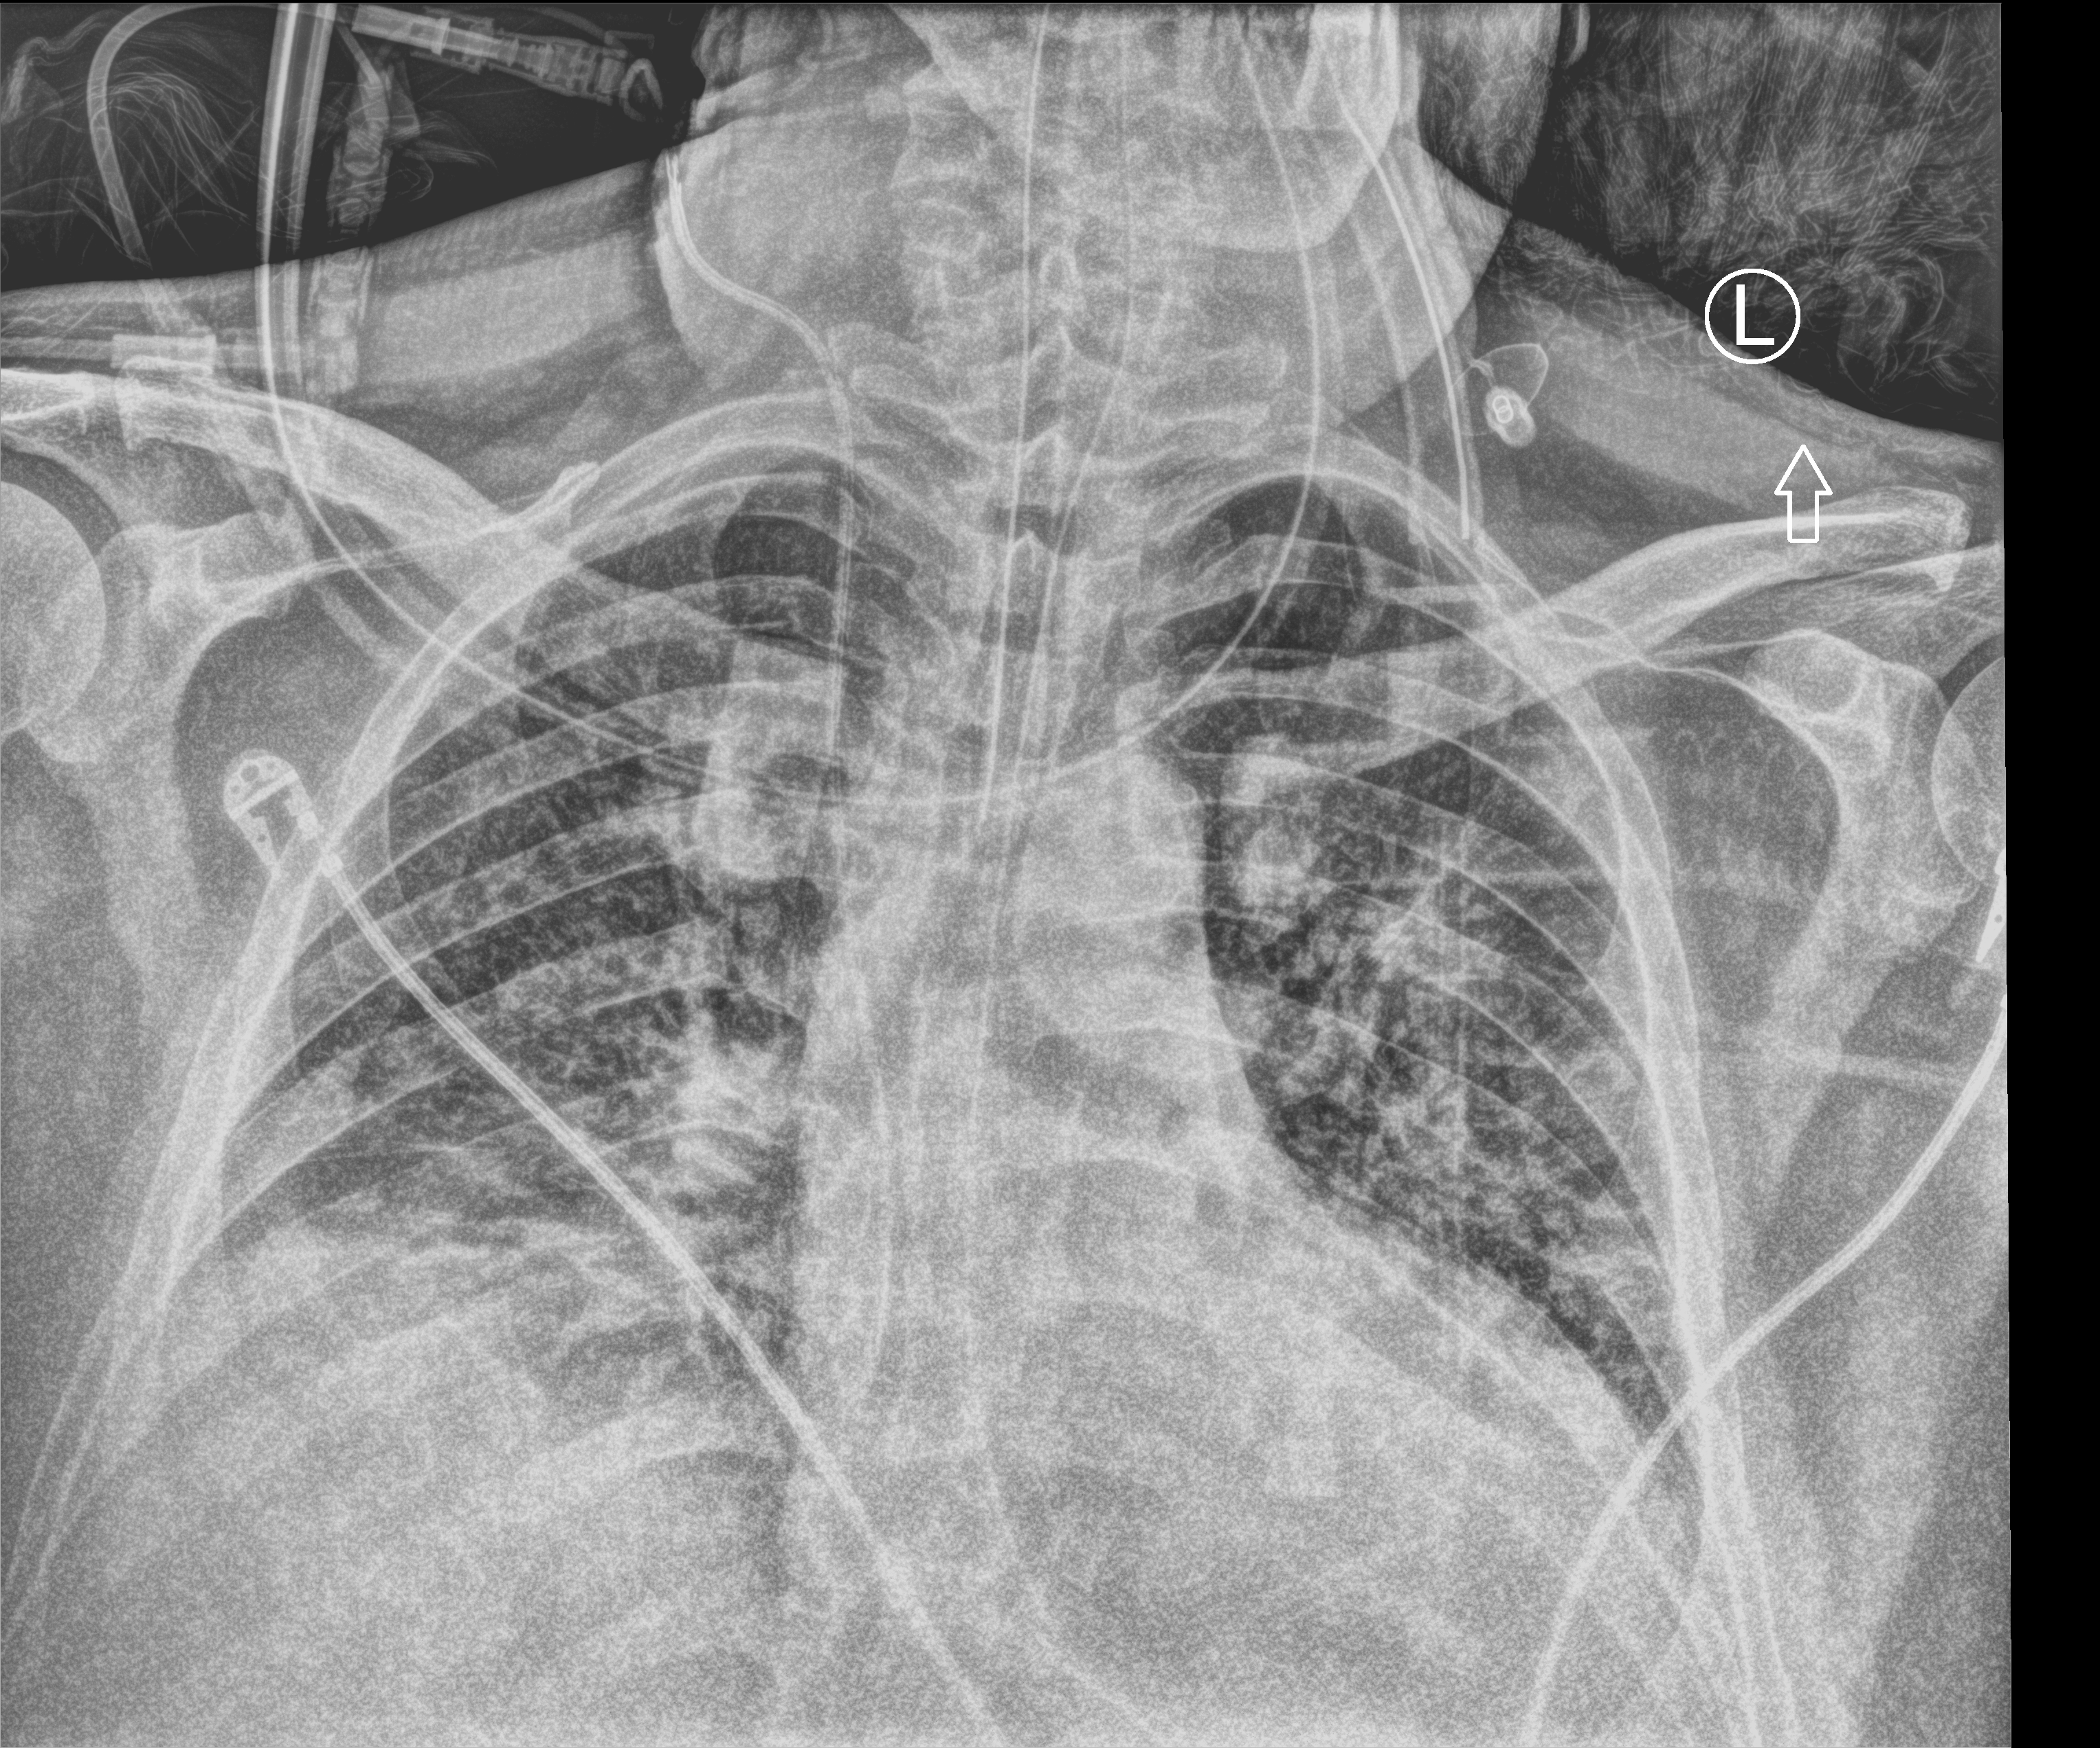
Chest X-ray (portable); anteroposterior (AP) projection. Patient hospitalised with COVID-19; male, aged 18–59 years.
From the hospital-stay record, not from the radiograph (when in the stay this image was taken is not recorded): admitted to intensive care during this hospital stay: yes; mechanically ventilated during this hospital stay: yes; COPD (admission record): no.